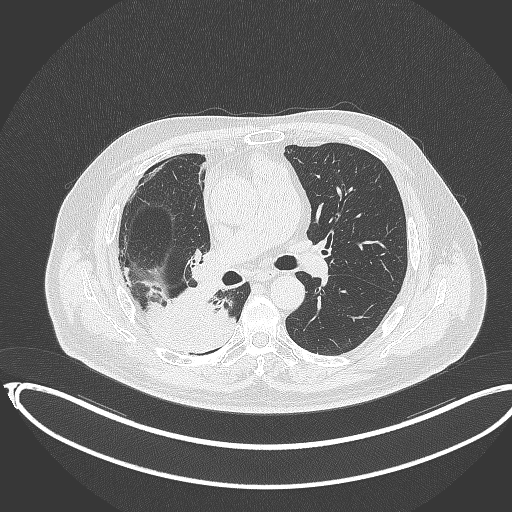
Chest CT, one axial slice; slice 202 of 403 in the series (ordered by position); 120 kVp; lung window (W 1500 / L -600 HU); 512 × 512 image matrix. Patient: male, 68 years. Case-level facts recorded for this patient, not image findings: clinical TNM (as recorded): T2a N0 M0.
Annotated regions visible in this slice (rectangle marked by the reading radiologist):
- lung tumour (recorded histology: adenocarcinoma): box from (x=141, y=284) to (x=234, y=350) px